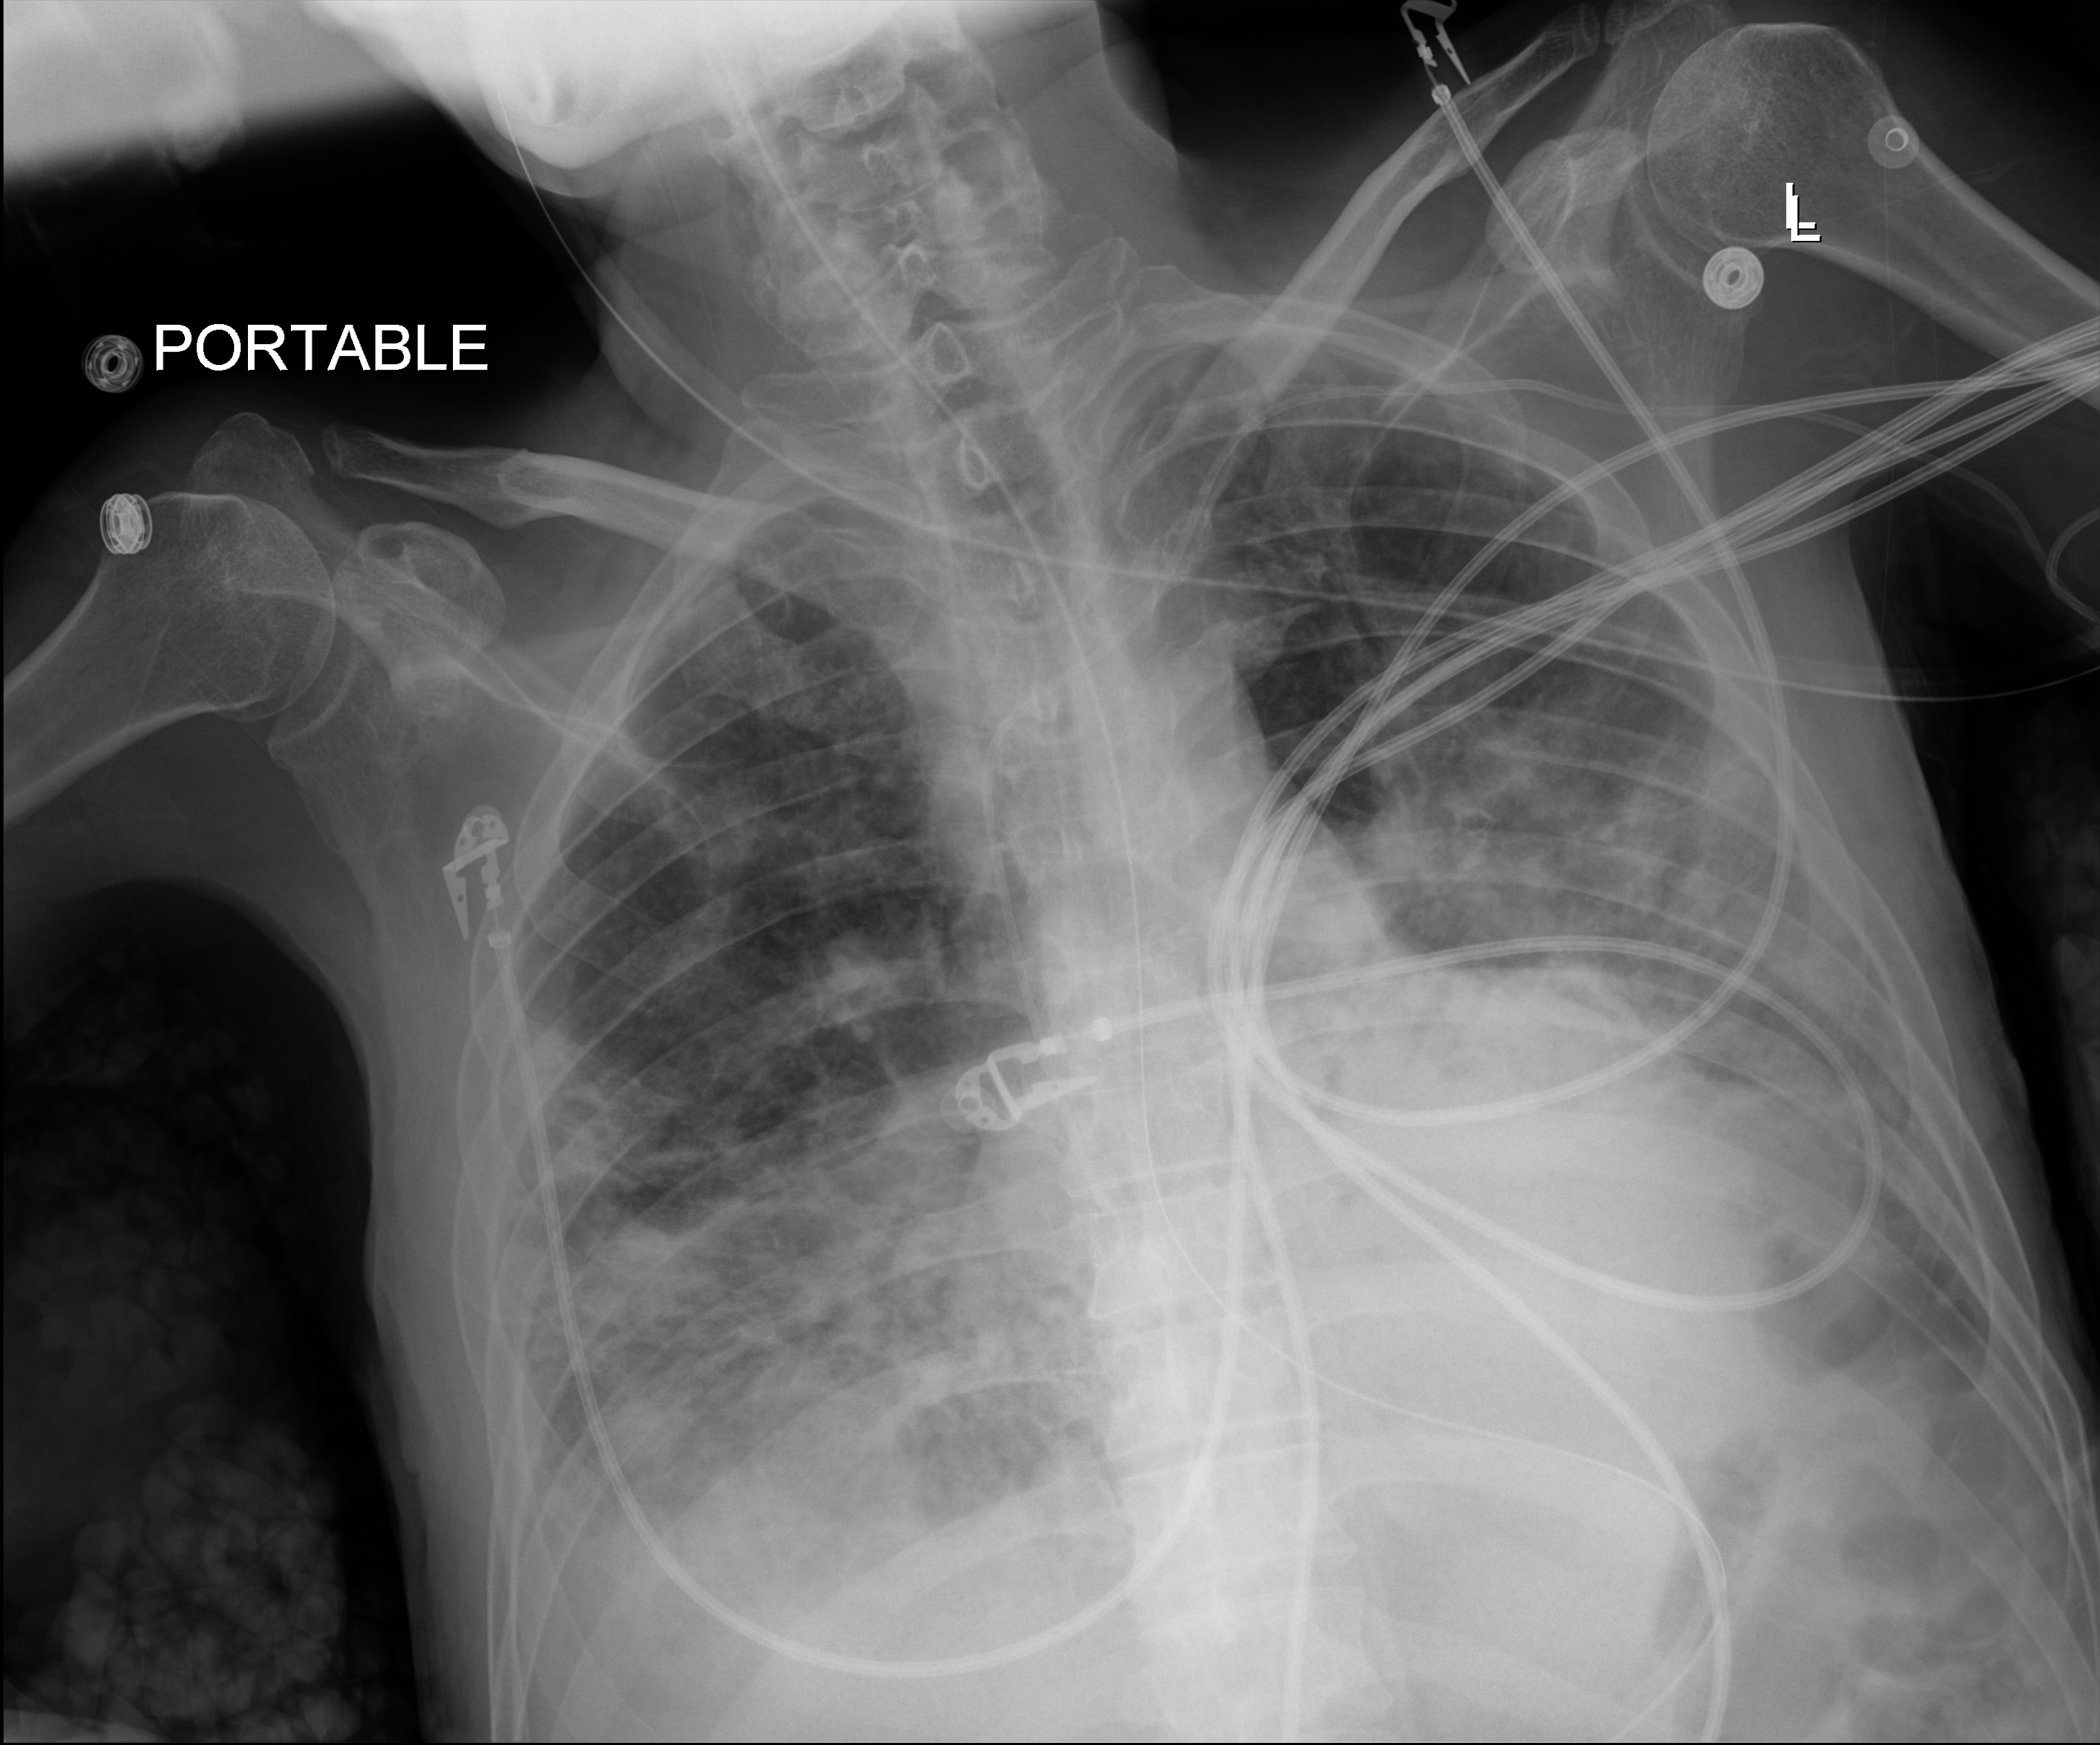
Chest radiograph (digital radiography), anteroposterior (AP) projection. Male patient hospitalised with COVID-19, age 18–59 years.
From the hospital-stay record, not from the radiograph (when in the stay this image was taken is not recorded):
- mechanically ventilated during this hospital stay: yes
- length of hospital stay: 96 days